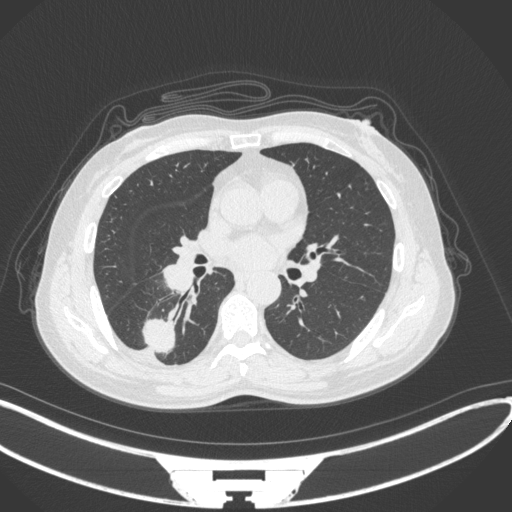
Chest CT, one axial slice. Slice 157 of 352 in the series (ordered by position). 120 kVp. Lung window (W 1500 / L -600 HU). 1 mm slice thickness. 512 × 512 image matrix, field of view 400 × 400 mm. Female patient, age 55 years. Case-level facts recorded for this patient, not image findings: clinical TNM (as recorded): T1c N1 M0.
Outlined on this slice (bounding box drawn by a radiologist):
- lung tumour (recorded histology: adenocarcinoma): bounding box <139,313,182,356> (left, top, right, bottom; pixels)